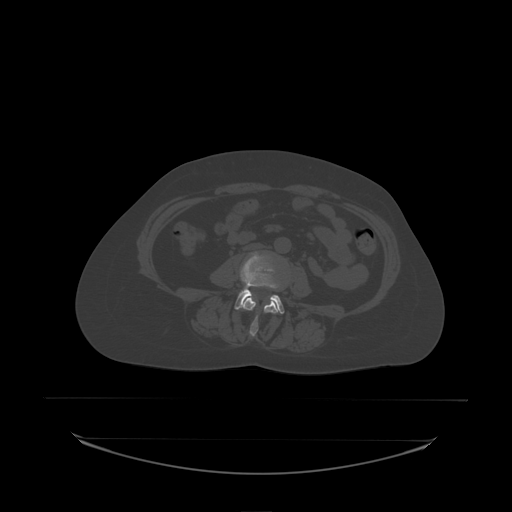
CT including the spine, one axial slice. Position 55 of 242 along the scan axis. Bone window (W 1800 / L 400 HU). 512 × 512 image matrix, field of view 500 × 500 mm. Female patient, age 53 years. From the clinical record (not read from this slice): primary cancer: lung; vertebrae with lytic lesions (as recorded): T7, L1.
Outlined on this slice (semi-automatic segmentation, software-assisted and operator-edited):
- L3 vertebra: bounding box [x1, y1, x2, y2] px = [243, 297, 278, 337]
- L4 vertebra: [235, 252, 285, 314]